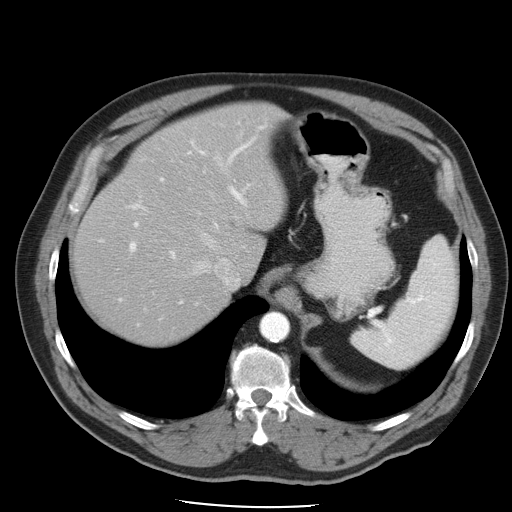
Contrast-enhanced abdominal CT, one axial slice; slice 37 of 49 in the series (ordered by position); intravenous contrast given; soft-tissue window (W 400 / L 40 HU); 5 mm slice thickness; 512 × 512 image matrix. Male patient, age 68 years. Case-level facts recorded for this patient, not image findings: diagnosis: colorectal cancer liver metastases, imaged before liver resection; multiple liver metastases: yes; largest metastasis: 1.7 cm; disease in both lobes: no.
Structures marked on this image (outlined manually by an expert reader):
- hepatic veins: bounding box (x1, y1, x2, y2) in pixels: (185, 156, 240, 288)
- liver: (72, 103, 286, 347)
- planned liver remnant (the part of the liver to remain after resection): (72, 103, 286, 346)
- portal vein (with intrahepatic branches): (100, 123, 266, 326)